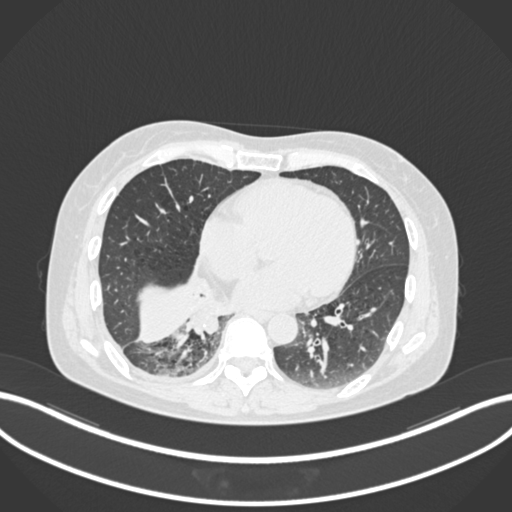
Chest CT, one axial slice. Slice 58 of 168 in the series (ordered by position). Reconstruction kernel B30f. 120 kVp. Lung window (W 1500 / L -600 HU). 1 mm slice thickness. 512 × 512 image matrix, field of view 400 × 400 mm. Patient: female, 63 years. From the clinical record (not read from this slice): clinical TNM (as recorded): T1c N0 M0.
Outlined on this slice (bounding box drawn by a radiologist):
- lung tumour (recorded histology: adenocarcinoma): bounding box [x1, y1, x2, y2] px = [183, 306, 228, 339]